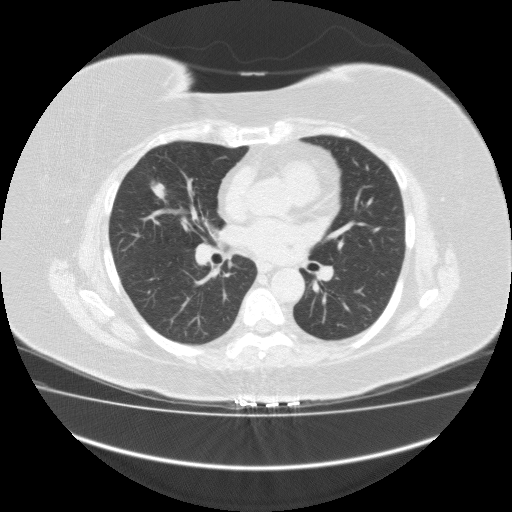
Low-dose screening chest CT, one axial slice. Slice 88 of 162 in the series (ordered by position). 120 kVp. Lung window (W 1500 / L -600 HU). 512 × 512 image matrix.
Outlined on this slice (manually delineated by an expert):
- lesion 1 (tumor, middle lobe of right lung): bounding box [x1, y1, x2, y2] px = [150, 179, 166, 200]